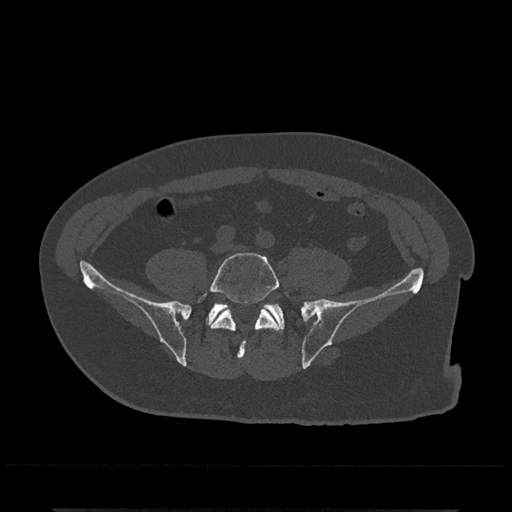
CT including the spine, one axial slice; slice 73 of 797 in the series (ordered by position); 120 kVp; bone window (W 1800 / L 400 HU); 0.5 mm slice thickness; 512 × 512 image matrix, field of view 393 × 393 mm. Patient: male, 67 years. From the clinical record (not read from this slice): primary cancer: prostate.
Structures marked on this image (semi-automatic segmentation, software-assisted and operator-edited):
- L5 vertebra: bounding box (x1, y1, x2, y2) in pixels: (198, 252, 287, 360)